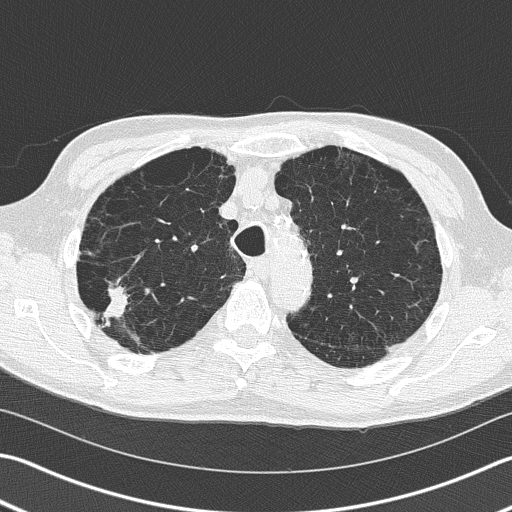
Low-dose screening chest CT, one axial slice; position 120 of 163 along the scan axis; 120 kVp; lung window (W 1500 / L -600 HU); 2 mm slice thickness; 512 × 512 image matrix, field of view 346 × 346 mm.
Structures marked on this image (expert manual segmentation):
- lesion 1 (tumor, upper lobe of right lung): box from (x=103, y=285) to (x=128, y=324) px